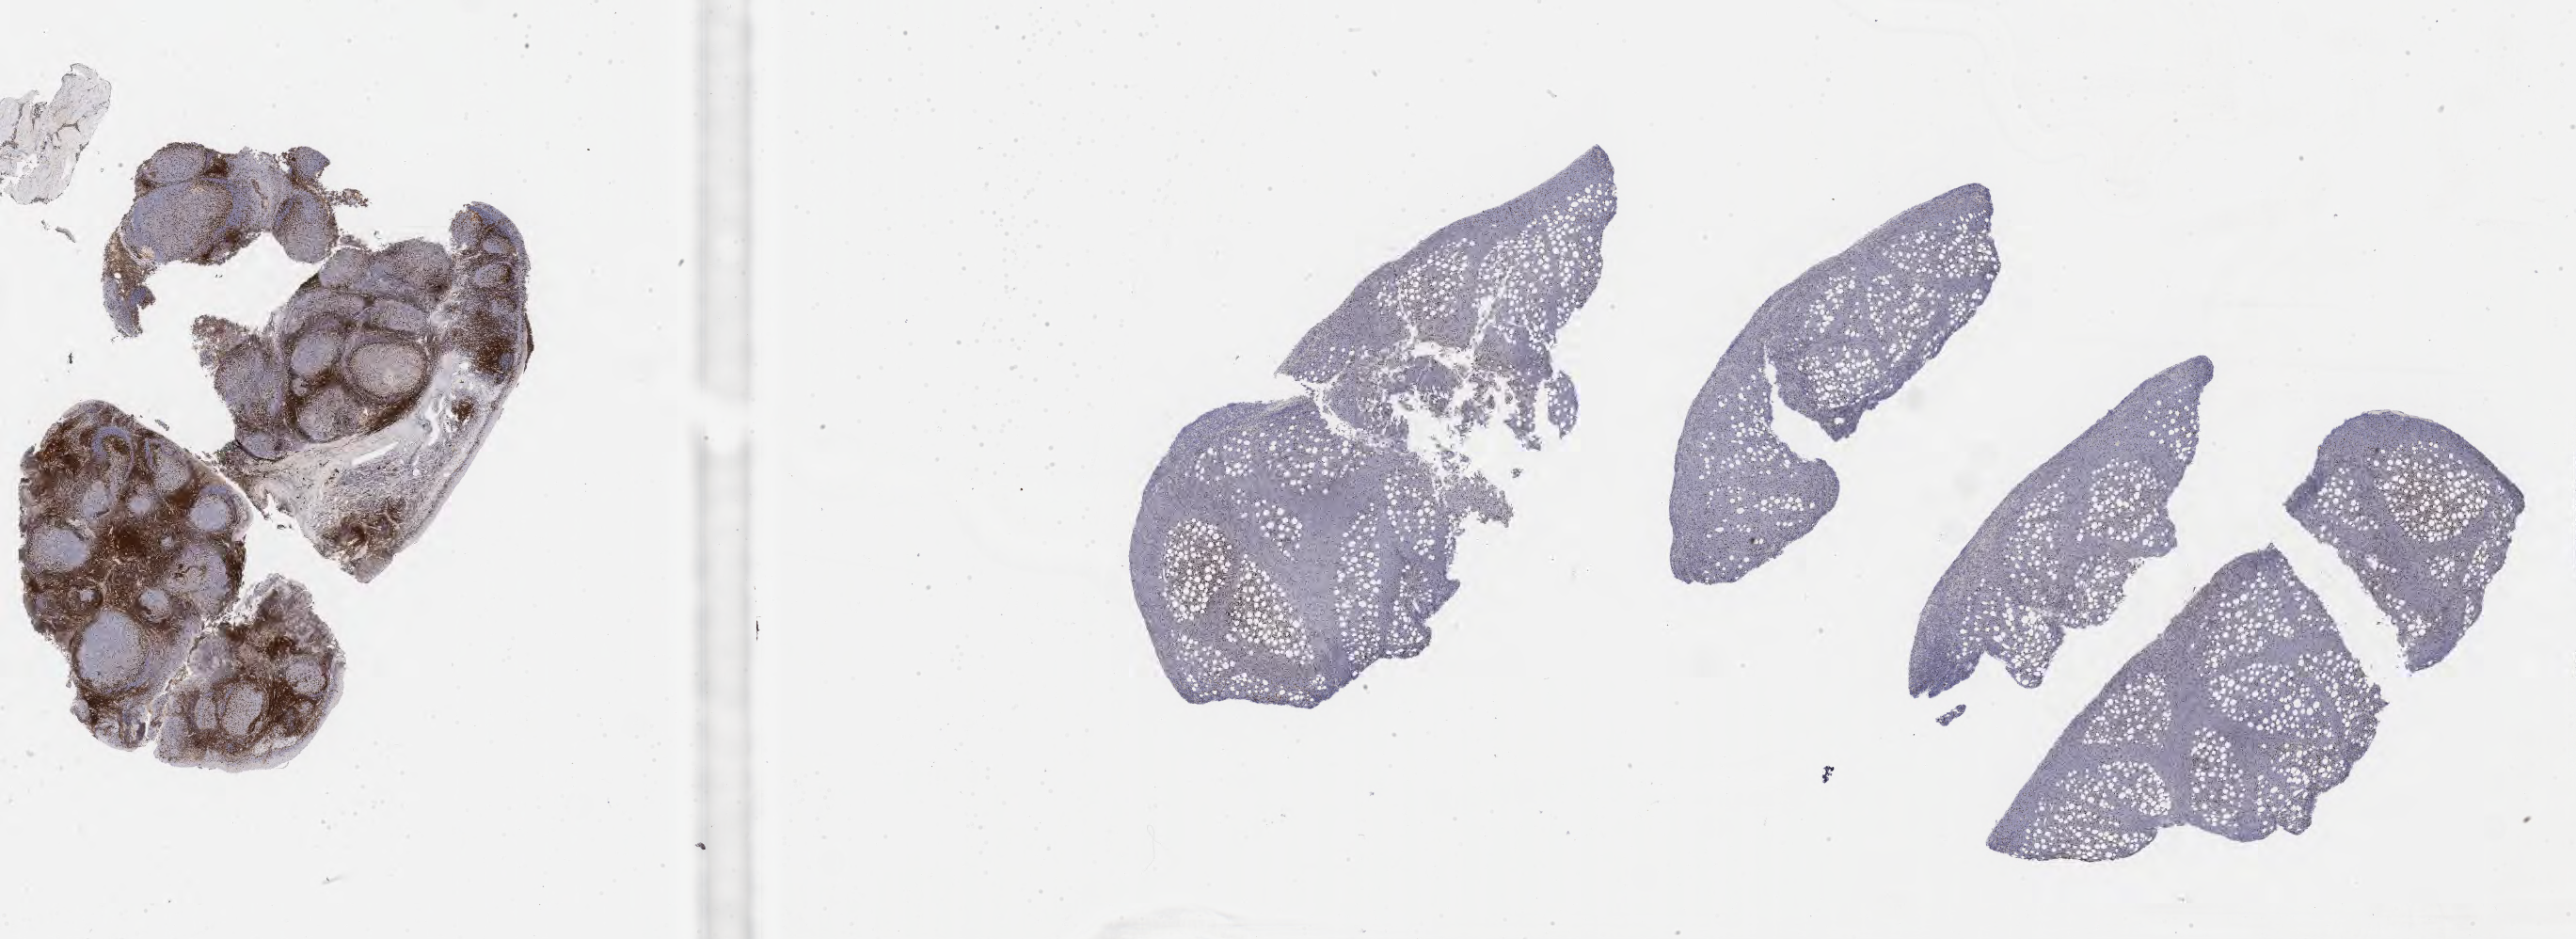
IHC for CD3, whole-slide image — shown as a low-resolution overview of the whole scanned area (about 44.3 x 16.1 mm), specimen: tumor tissue. Patient: male, aged 52.
Diagnosis: Diffuse large B-cell lymphoma, NOS.